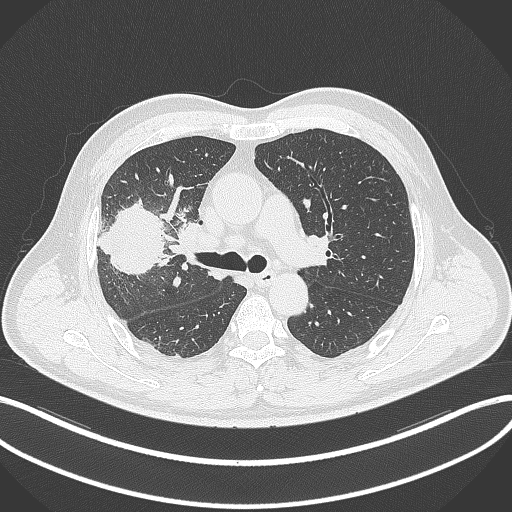
Chest CT, one axial slice; position 211 of 348 along the scan axis; 120 kVp; lung window (W 1500 / L -600 HU); 512 × 512 image matrix, field of view 400 × 400 mm. Male patient, age 55 years. From the clinical record (not read from this slice): clinical TNM (as recorded): T3 N2 M1.
Outlined on this slice (rectangle marked by the reading radiologist):
- lung tumour (recorded histology: adenocarcinoma): bounding box [x1, y1, x2, y2] px = [98, 198, 164, 277]